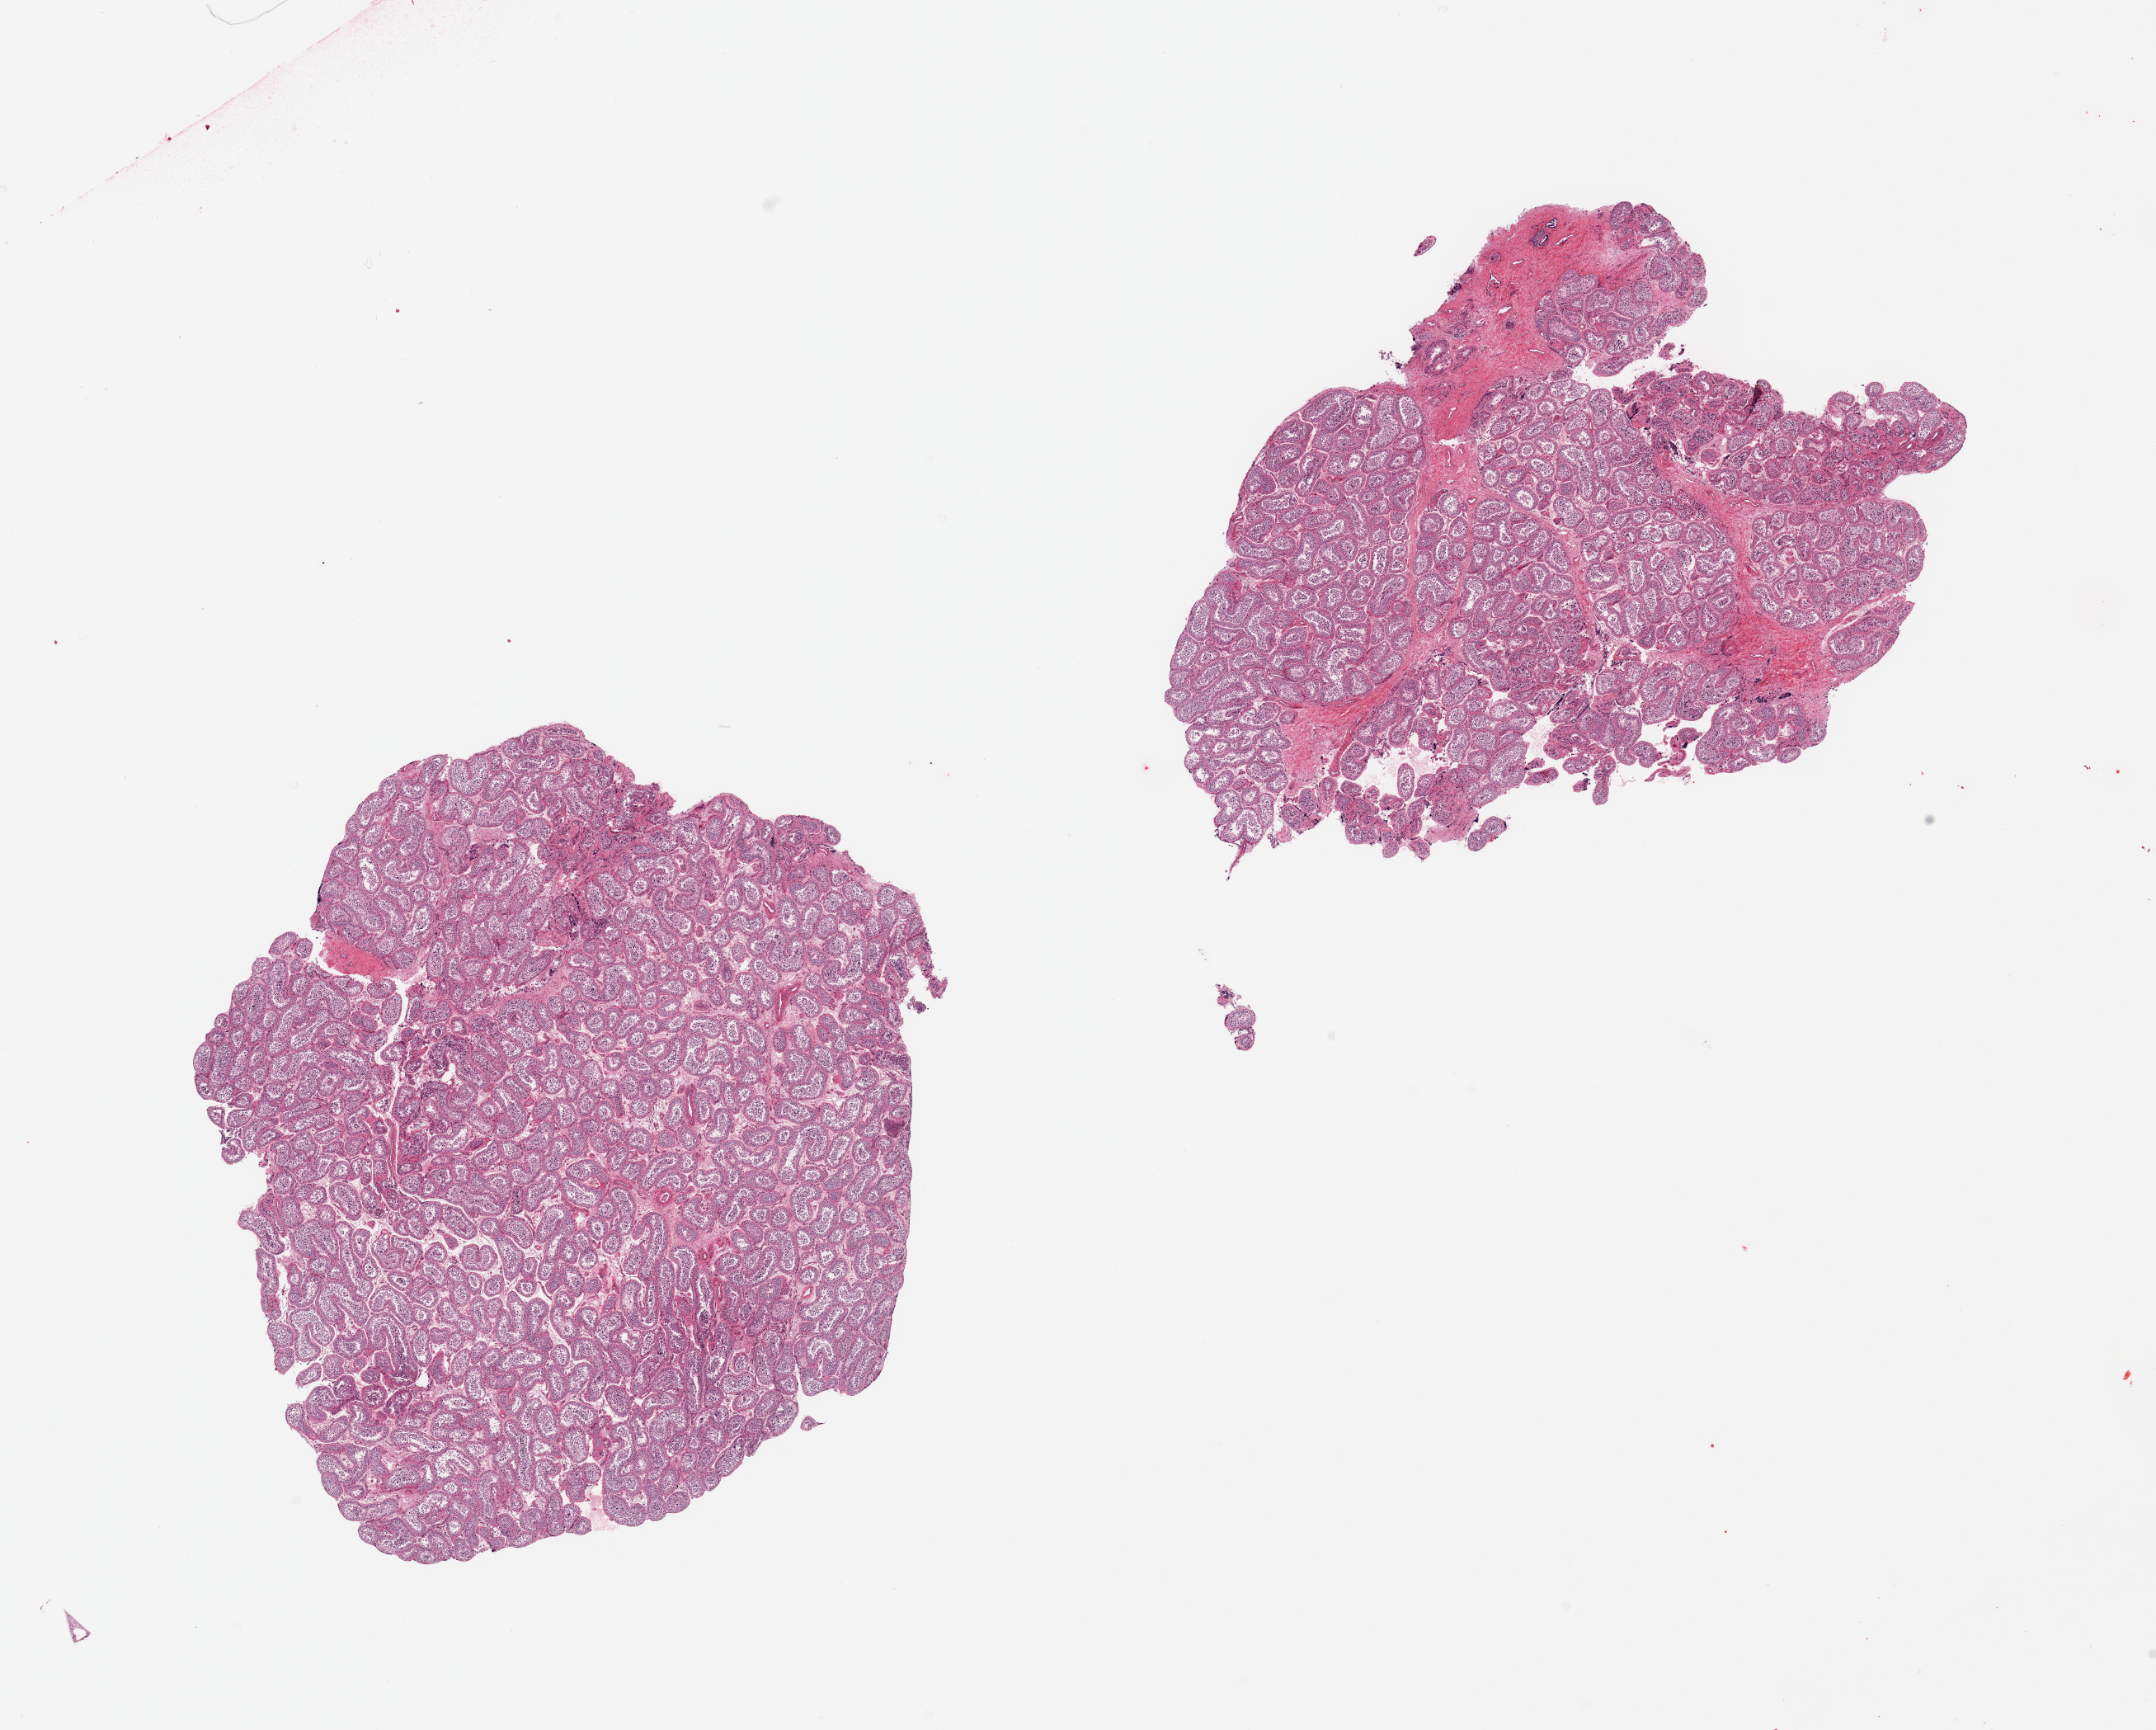
Digitized H&E-stained section — a low-resolution overview of the entire scanned area, about 20.7 x 16.6 mm; PAXgene-fixed, paraffin-embedded tissue; section of testis (target tissue); tissue donor sample. Donor: male.
- pathologist's review note for this sample: 2 pieces; spermatogenesis is present